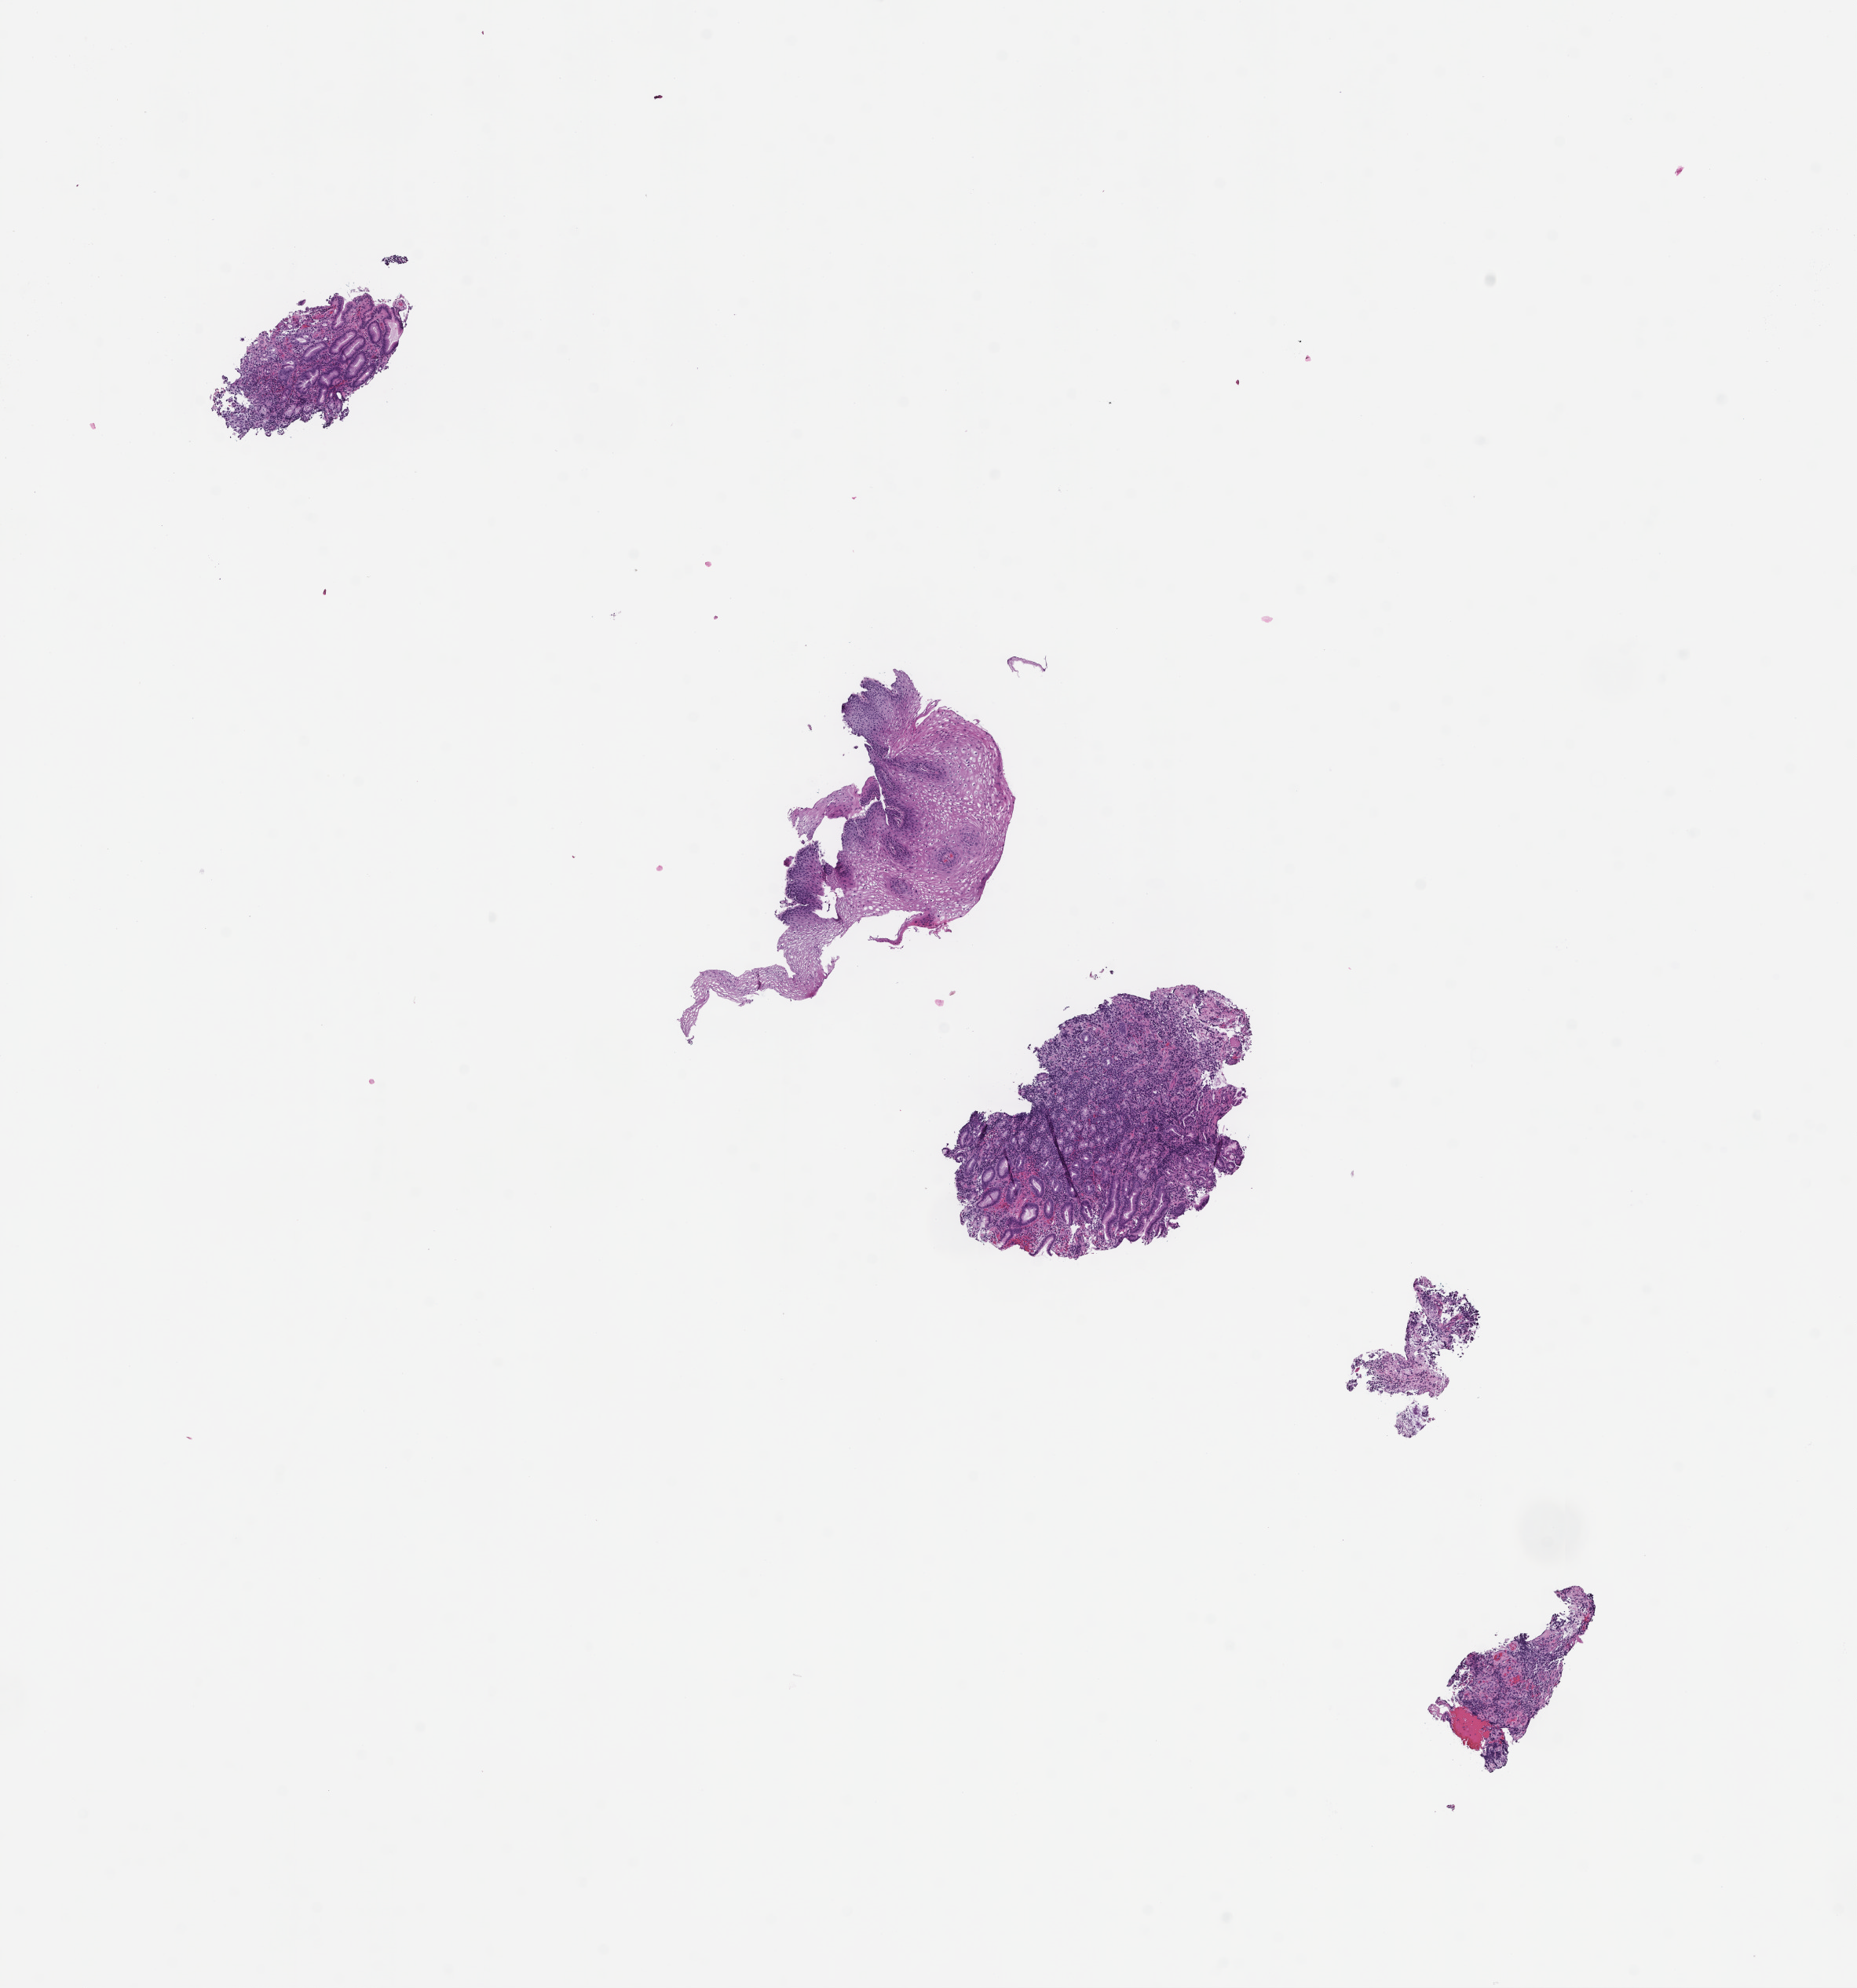
Digitized haematoxylin and eosin-stained section, shown as a low-resolution overview of the whole scanned area (about 9.5 x 10.2 mm); formalin-fixed, paraffin-embedded (FFPE) tissue; site: esophagus; archival tissue. Patient: male.
This section: primary tumour tissue. Diagnosis: Gastric Carcinoma.